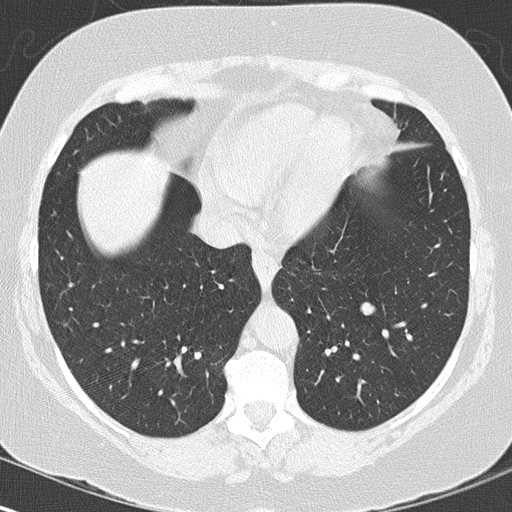
Chest CT (low-dose screening protocol), one axial image. Baseline screening round. Lung window (W 1500 / L -600 HU). 2 mm slice thickness. Female participant, aged 60 years at enrolment. Former smoker at enrolment.
Expert-annotated lung lesion, bounding box [x1, y1, x2, y2] px = [349, 290, 391, 331]. Reader record for this screening exam (exam-level; its link to the box is not recorded): non-calcified nodule or mass ≥4 mm, left lower lobe, 12 × 10 mm, smooth margins, soft tissue attenuation. Official screen result: positive, change unspecified: nodule(s) >= 4 mm or enlarging nodule(s), mass(es), or other non-specific abnormalities suspicious for lung cancer. Lung cancer was diagnosed 109 days after this screen: carcinoid tumor, NOS, left lower lobe, carcinoid, stage not assessed, 13 mm at pathology.